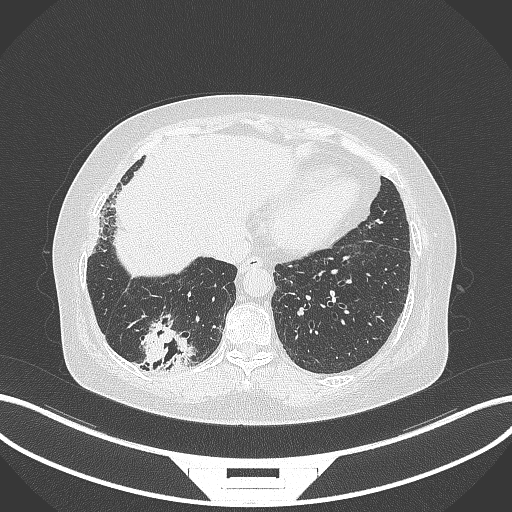
Chest CT, one axial slice; slice 46 of 296 in the series (ordered by position); reconstruction kernel B70f; 120 kVp; lung window (W 1500 / L -600 HU); 1 mm slice thickness; 512 × 512 image matrix, field of view 400 × 400 mm. Female patient, age 65 years. Case-level facts recorded for this patient, not image findings: clinical TNM (as recorded): T2b N1 M0; histopathological grade: G1.
Annotated regions visible in this slice (rectangle marked by the reading radiologist):
- lung tumour (recorded histology: adenocarcinoma): bounding box <135,311,199,376> (left, top, right, bottom; pixels)